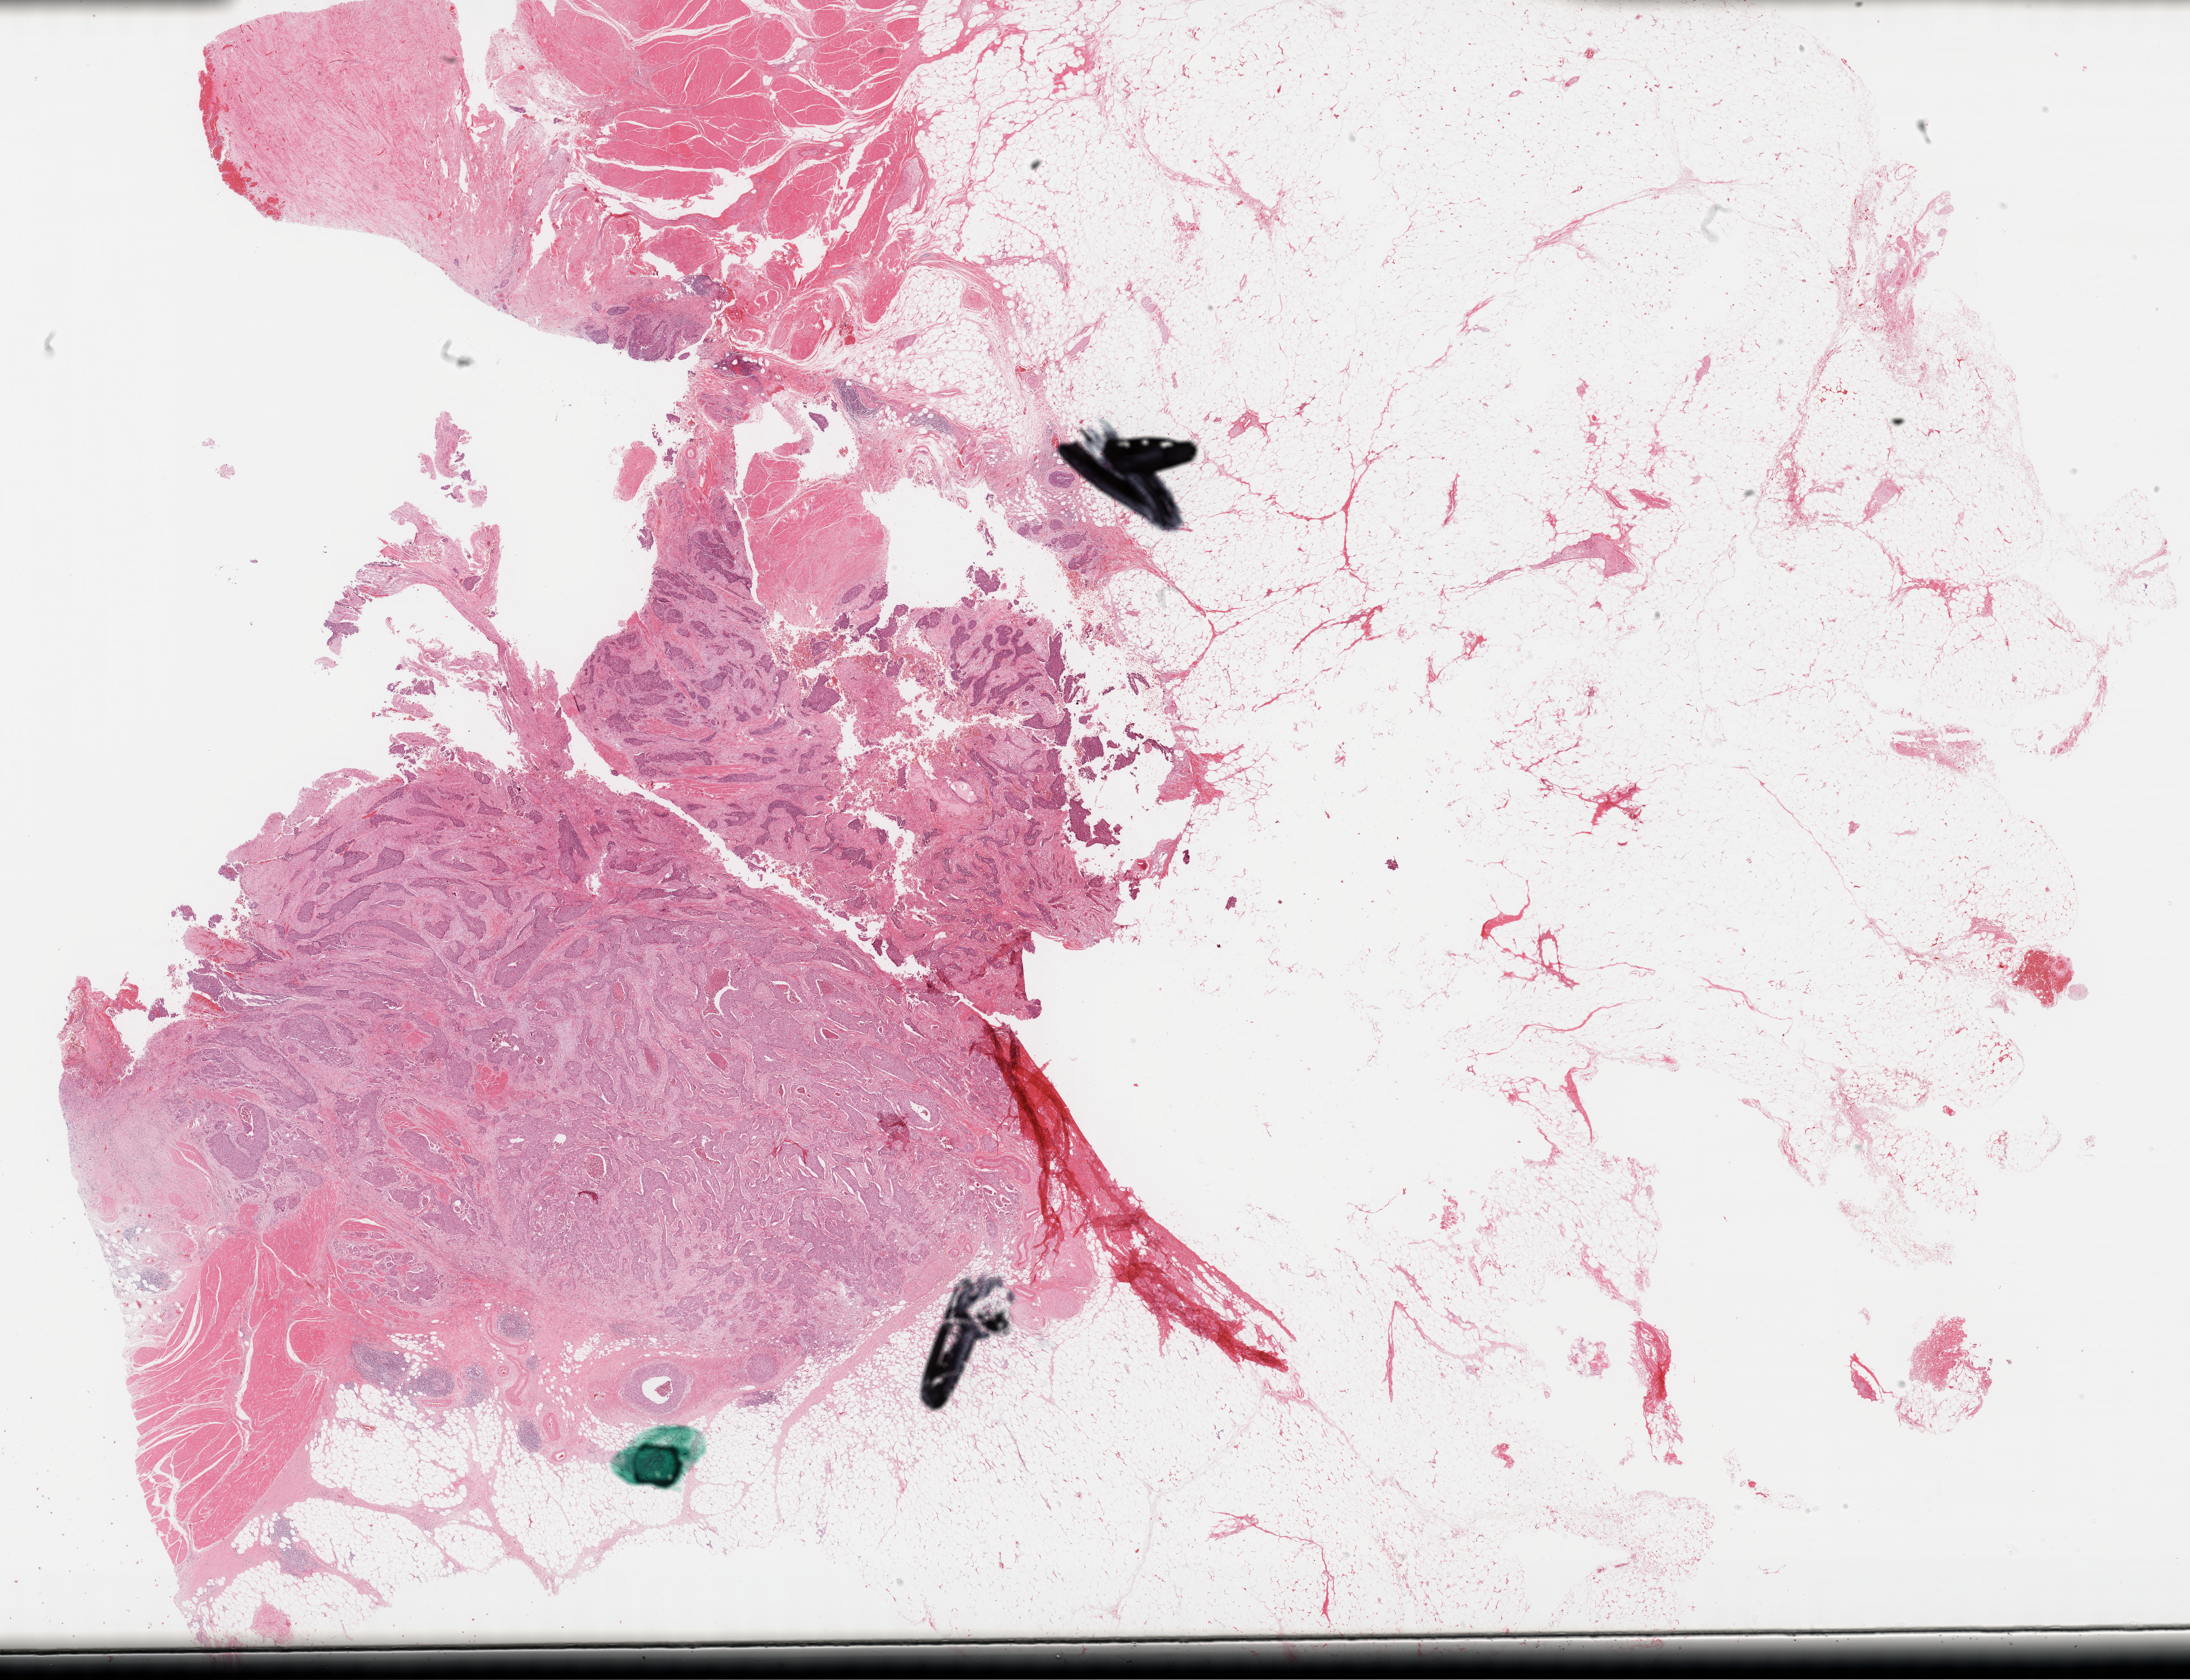
Whole-slide histology image, Hematoxylin and eosin (H&E) stained, low-resolution overview of the scanned area, about 31.2 x 23.9 mm (from a 40x scan), formalin-fixed paraffin-embedded (FFPE) diagnostic section, primary tumour sample from the bladder. Male, age 67 years at initial diagnosis. Histologic grade: high grade.
* lymph nodes positive (case pathology): 2 of 6 examined
* histologic diagnosis: Transitional cell carcinoma
* AJCC pathologic stage: IV